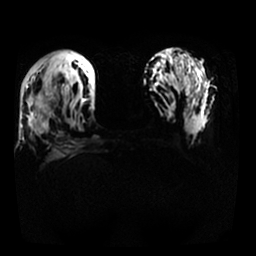
Breast MRI, one axial slice; slice 13 of 25 in the series (ordered by position); diffusion-weighted series; image 2 of 4 stored at this slice position (different b-values; order by instance number); 1.5 T; 4 mm slice thickness; 256 × 256 image matrix, field of view 340 × 340 mm. Female patient.
Annotated regions visible in this slice (outlined manually by an expert reader):
- tumour on diffusion-weighted imaging: bounding box <29,86,57,115> (left, top, right, bottom; pixels)